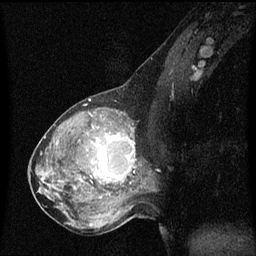
Breast MRI (dynamic contrast-enhanced), one sagittal slice; position 30 of 60 along the scan axis; dynamic contrast-enhanced series, image 2 of 3 at this slice position (ordered by acquisition); 1.5 T; TE 4.2 ms, TR 8 ms; 256 × 256 image matrix. Patient: female, 50 years.
Annotated regions visible in this slice (semi-automatic segmentation, software-assisted and operator-edited):
- analysis volume of interest (the breast-tissue region the enhancement analysis was run in; not a lesion): box from (x=91, y=126) to (x=141, y=189) px
- tumour enhancement mask (voxels above the 70 % enhancement threshold inside the analysis volume of interest): (x=91, y=134)–(x=135, y=181)